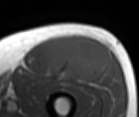
MRI of an extremity soft-tissue mass, one axial slice; slice 46 of 86 in the series (ordered by position); MR volume resampled by the dataset authors to the PET/CT grid (not the native acquisition matrix); 3.27 mm slice thickness; 139 × 117 image matrix. Male patient. From the clinical record (not read from this slice): histological type: extraskeletal osteosarcoma; grade: high; site of the primary tumour: thigh.
Outlined on this slice (expert contour drawn on MRI and transferred to this co-registered scan by the dataset authors):
- gross tumour volume (mass): bounding box <49,36,107,81> (left, top, right, bottom; pixels)